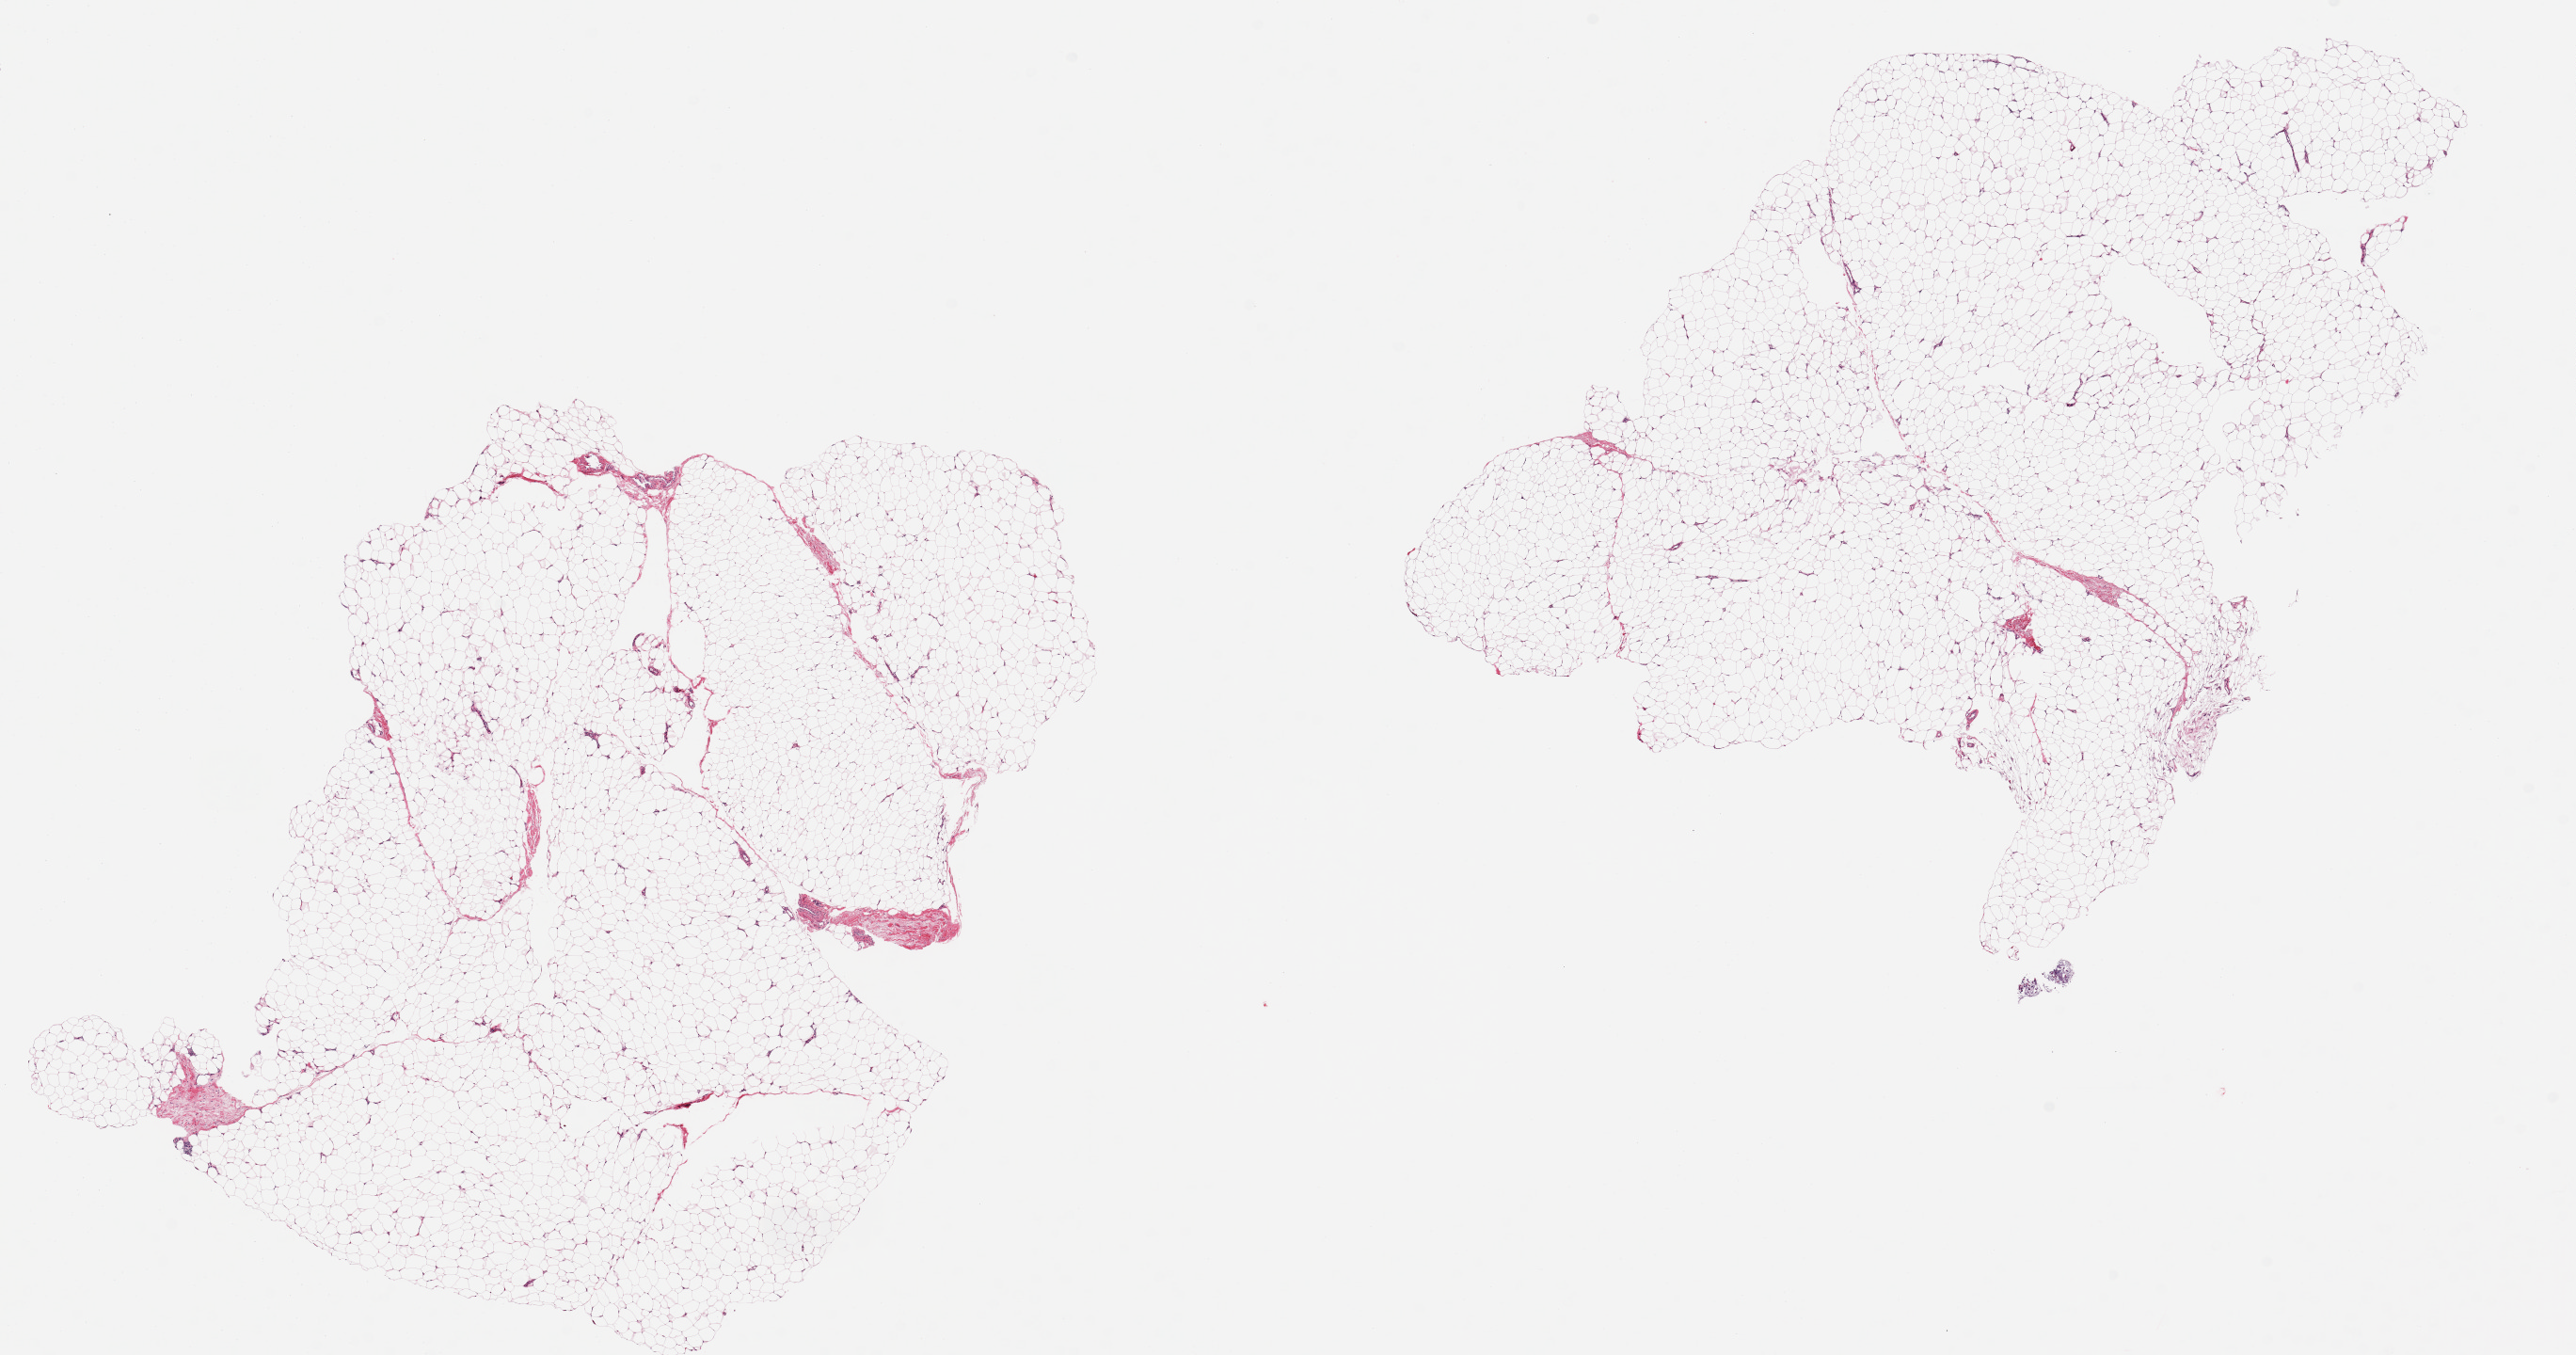
Digitized hematoxylin and eosin (H&E)-stained section — a low-resolution overview of the entire scanned area, about 21.7 x 11.4 mm (slide scanned at 20x), PAXgene-fixed paraffin-embedded (PFPE) section, target tissue: adipose tissue, donor tissue sample.
- reviewer comment on this tissue sample: 2 pieces, only trace fascia